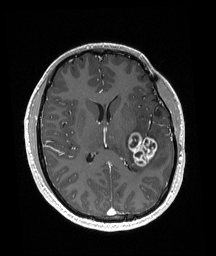
Brain MRI from a brain-tumour surgery series, one axial slice; slice 82 of 192 in the series (ordered by position); T1-weighted post-contrast; 1 mm slice thickness; 216 × 256 image matrix. Case-level facts recorded for this patient, not image findings: histopathology: Glioneuronal tumor; WHO grade: 2.
Structures marked on this image (outlined manually by an expert reader):
- tumour: bounding box (x1, y1, x2, y2) in pixels: (128, 132, 158, 167)